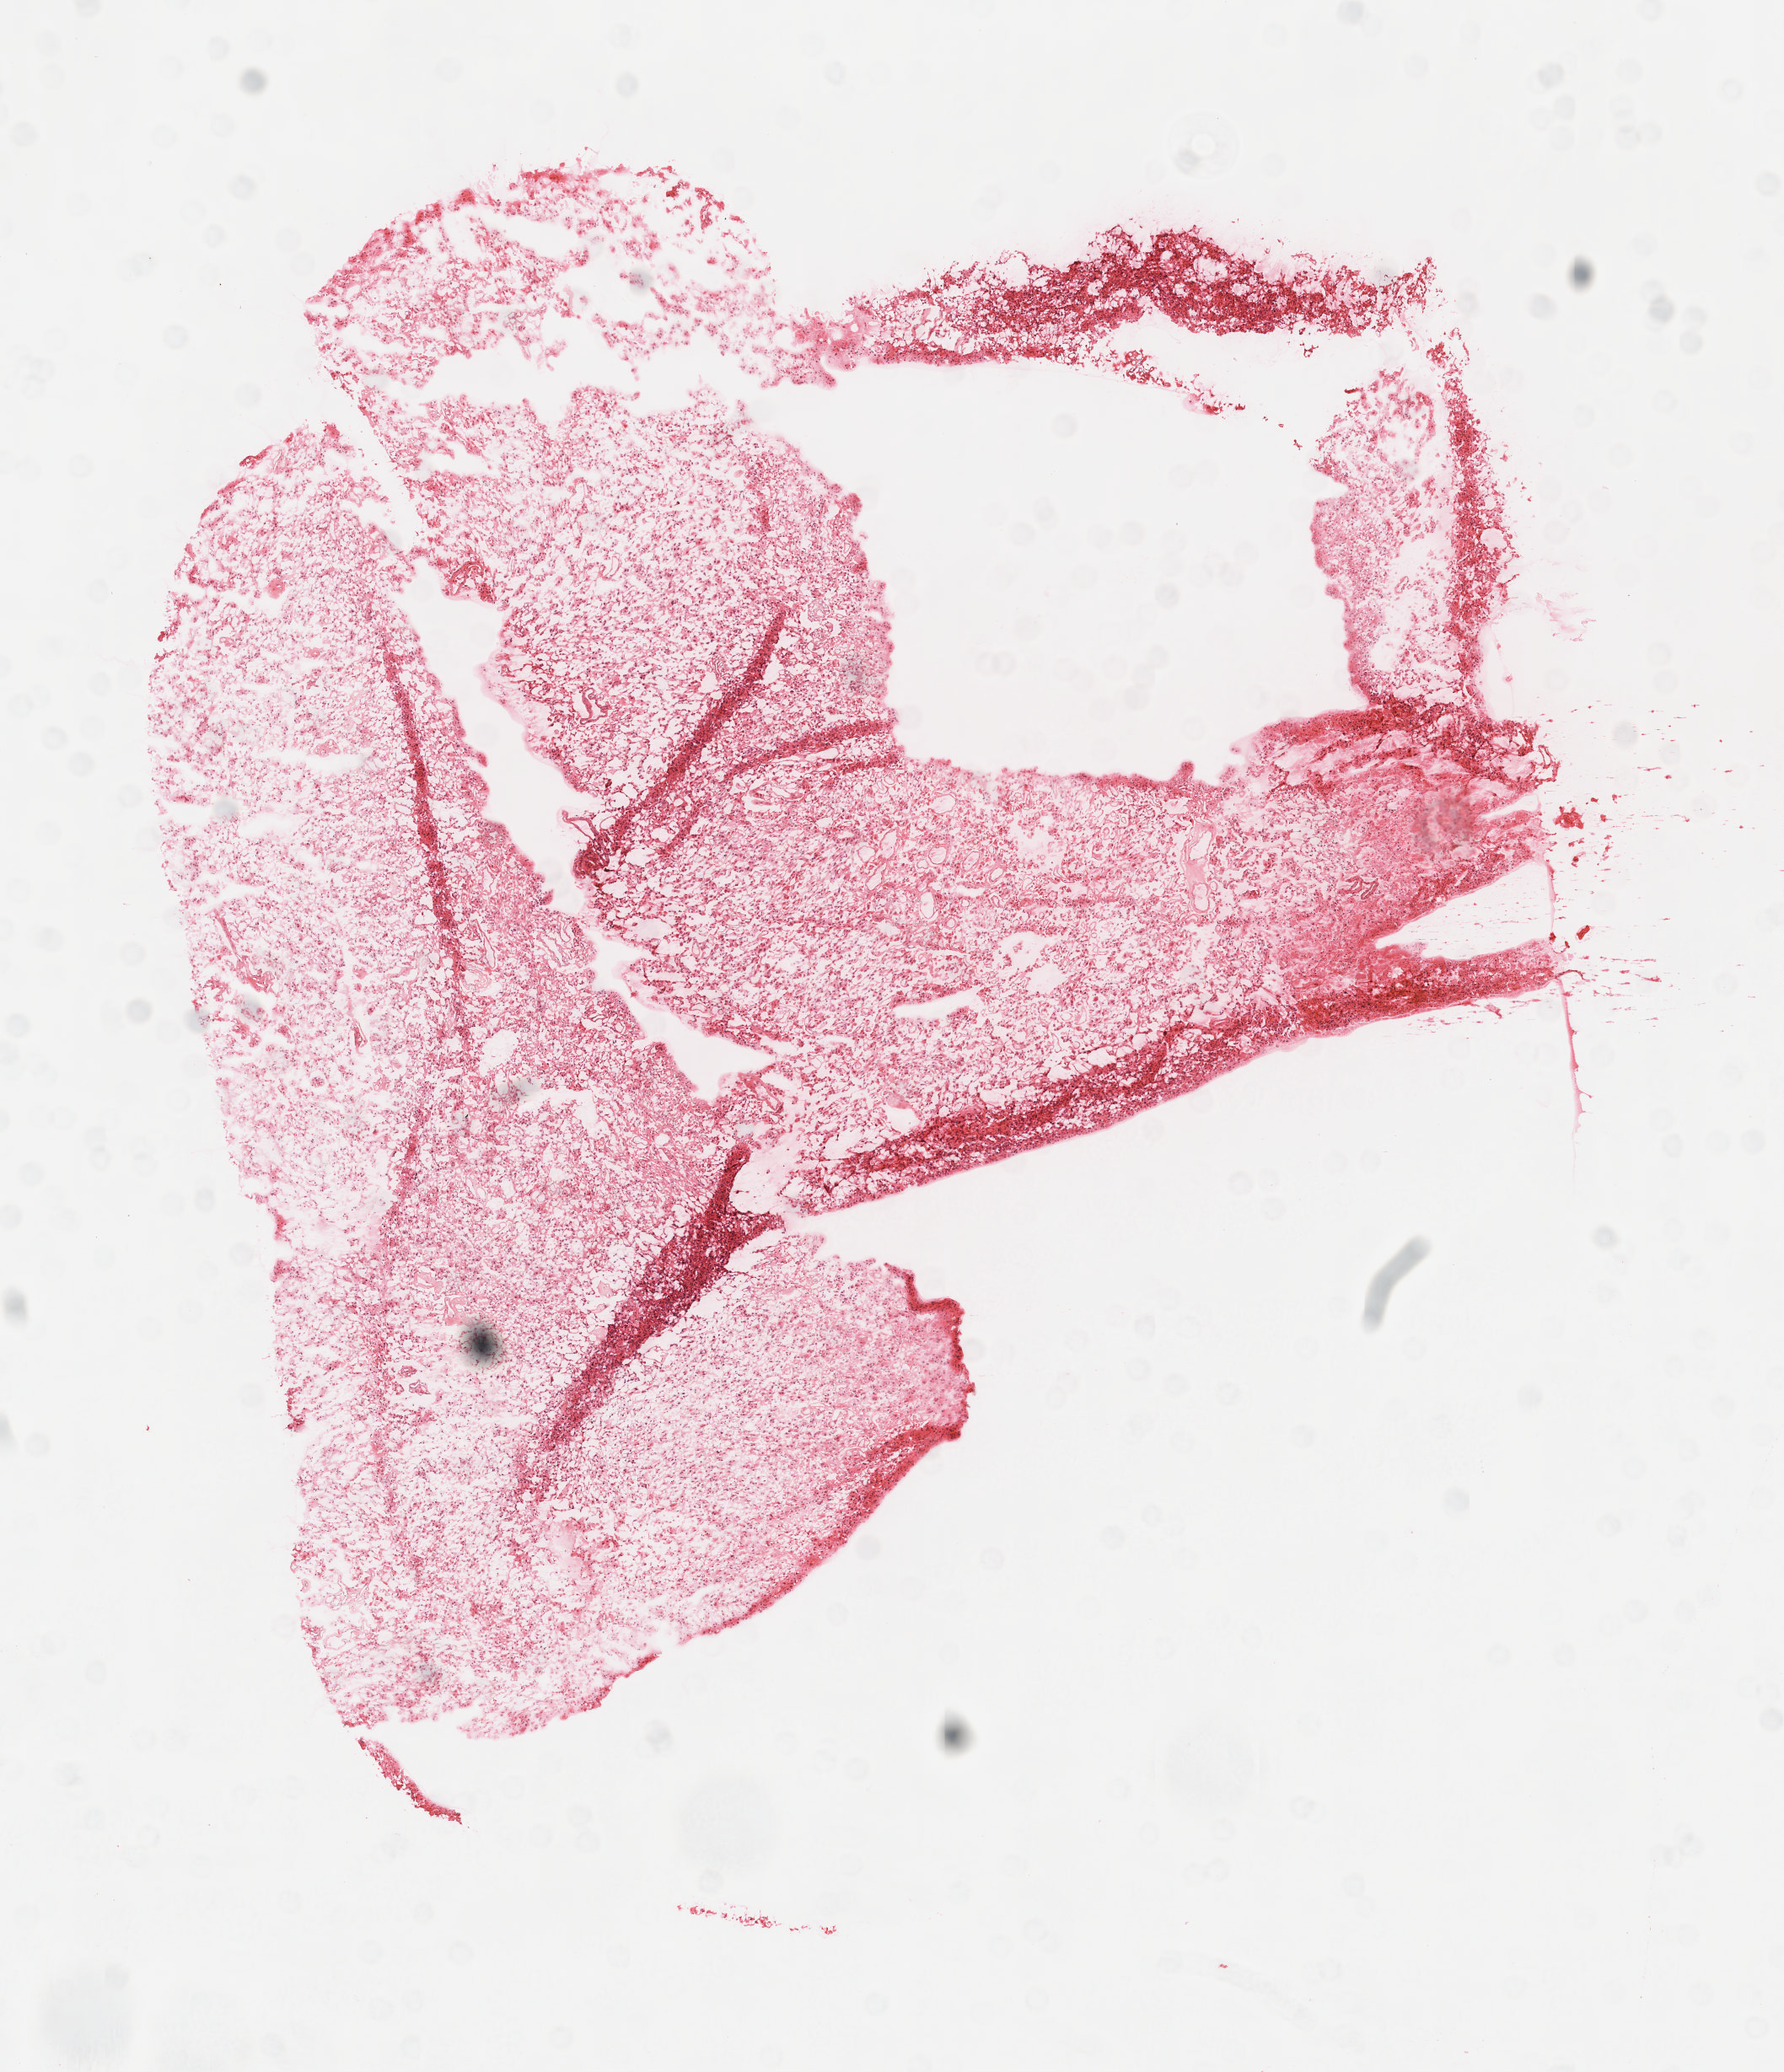
H&E-stained whole-slide image, whole scanned area (about 8.6 x 9.9 mm, from a 40x scan) shown as a low-resolution overview. Frozen section from the top of the tissue portion. Sample: primary tumour, brain. Female, age 45 years at initial diagnosis. Pathologist review of this section (percent, as recorded): tumour cells 95%, tumour nuclei 100%, normal cells 0%, stromal cells 0%, necrosis 5%. Infiltration values recorded for this section: lymphocyte infiltration 0%.
Diagnosis: Glioblastoma.